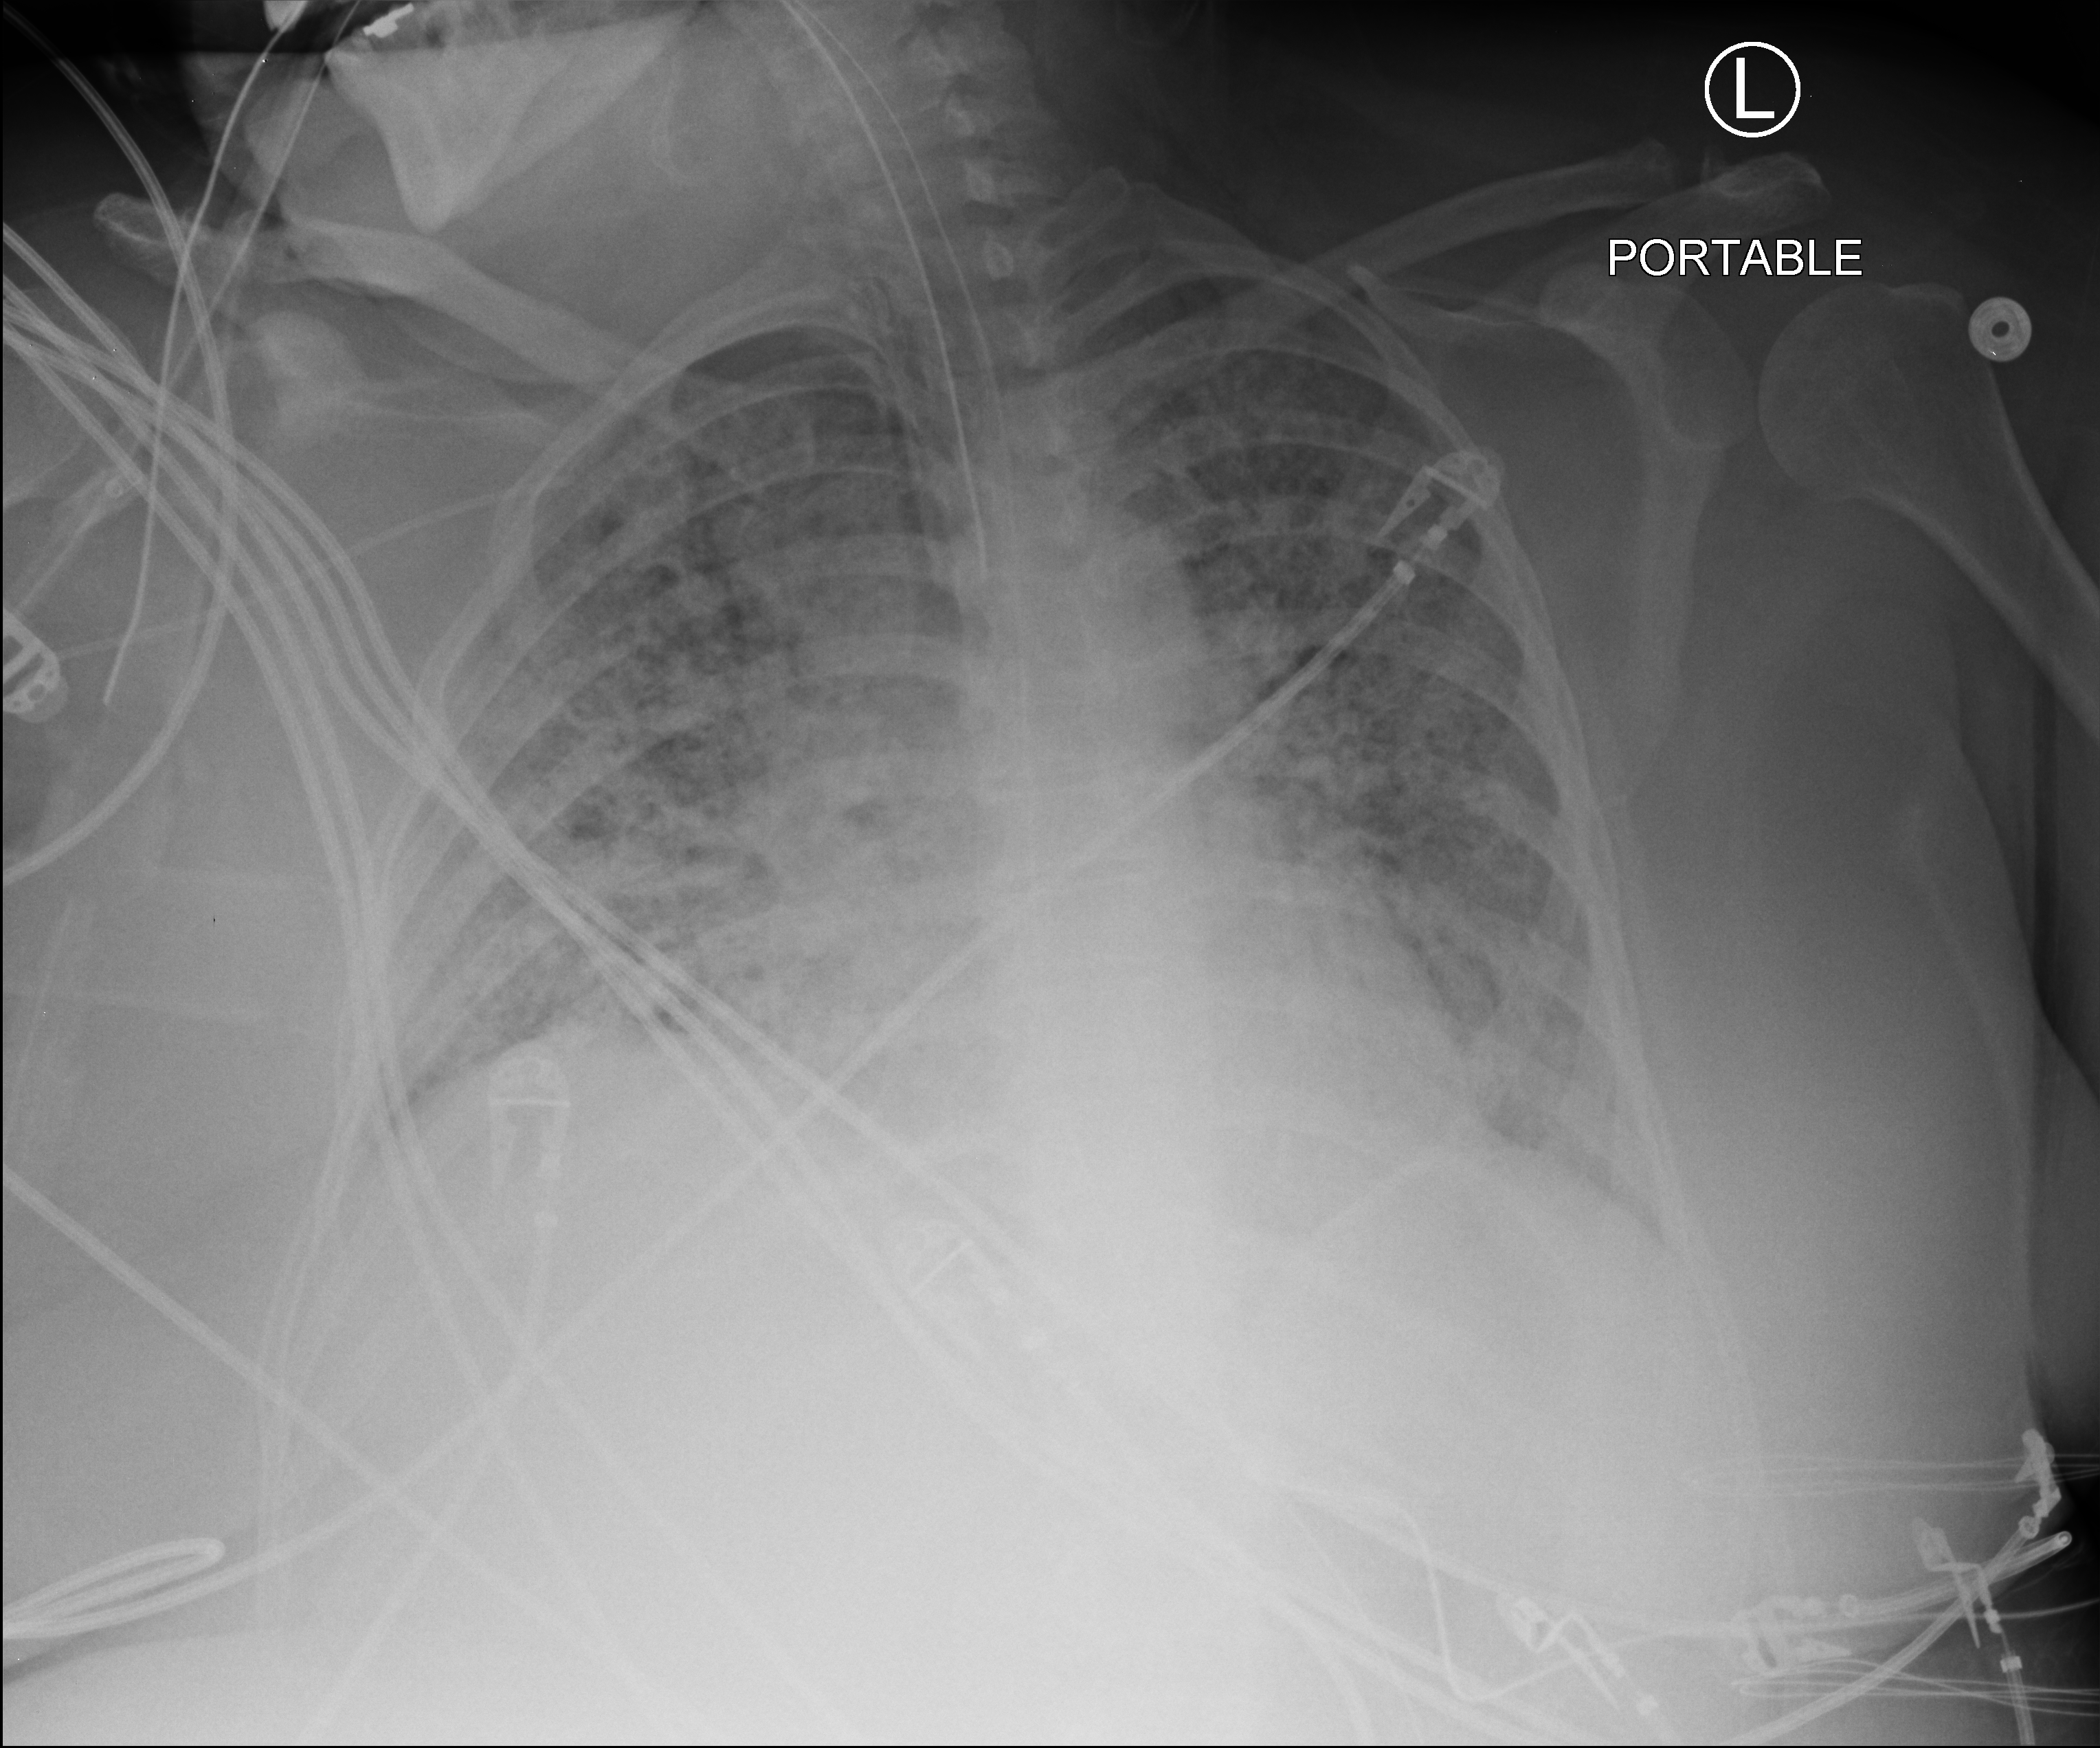
Bedside chest radiograph (computed radiography); anteroposterior (AP) projection. Female patient hospitalised with COVID-19, age 18–59 years.
From the hospital-stay record, not from the radiograph (when in the stay this image was taken is not recorded): other chronic lung disease (admission record): no.